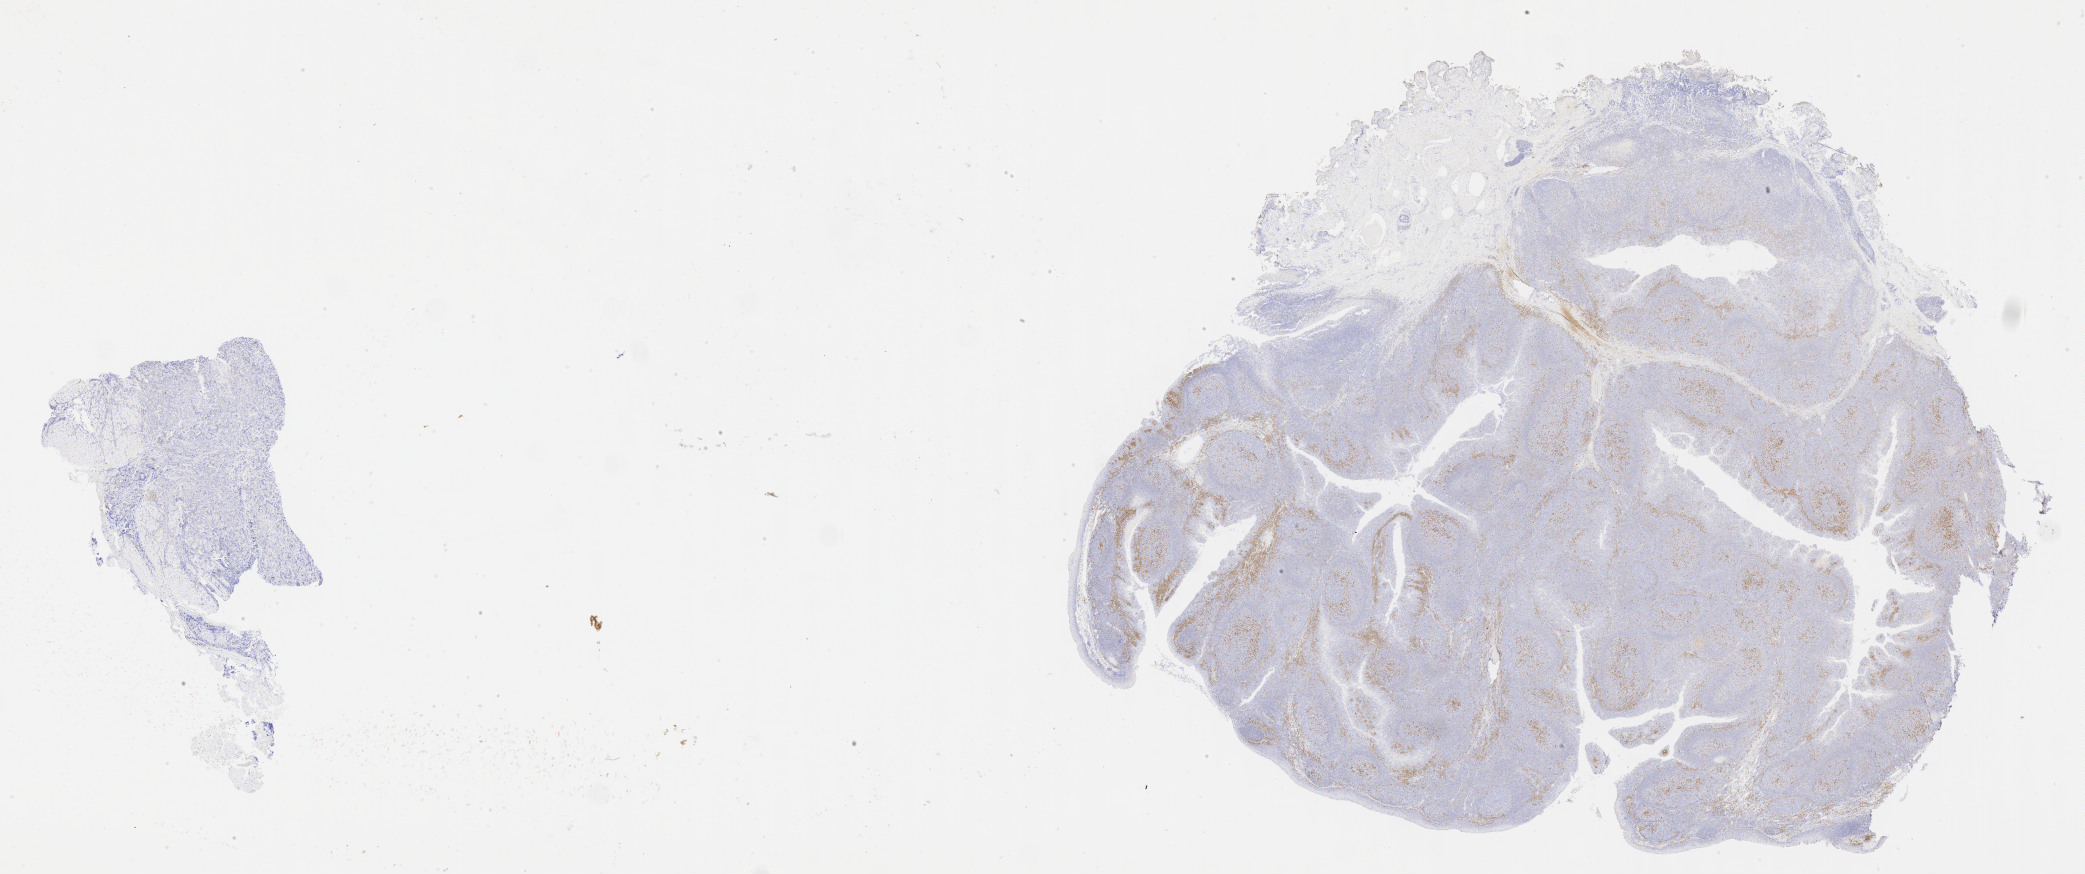
Whole-slide image, immunohistochemical stain for IRF4/MUM1 — a low-resolution overview of the entire scanned area, about 33.7 x 14.1 mm; specimen: tumor tissue; site: kidney. Male patient, 12 years old.
• histologic diagnosis: Diffuse large B-cell lymphoma, NOS